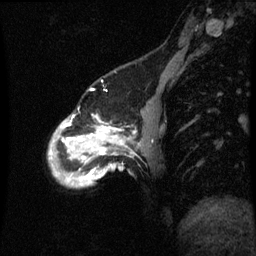
Breast MRI (dynamic contrast-enhanced), one sagittal slice. Position 13 of 60 along the scan axis. Dynamic contrast-enhanced series, image 2 of 3 at this slice position (ordered by acquisition). 1.5 T. TE 4.2 ms, TR 8.9 ms. 2 mm slice thickness. 256 × 256 image matrix, field of view 200 × 200 mm. Female patient, age 49 years. Case-level facts recorded for this patient, not image findings: setting: breast cancer imaged before/during neoadjuvant chemotherapy; receptor status: HR-positive, HER2-negative.
Structures marked on this image (semi-automatic segmentation, software-assisted and operator-edited):
- analysis volume of interest (the breast-tissue region the enhancement analysis was run in; not a lesion): bounding box (x1, y1, x2, y2) in pixels: (50, 114, 143, 189)
- tumour enhancement mask (voxels above the 70 % enhancement threshold inside the analysis volume of interest): (62, 128, 123, 171)